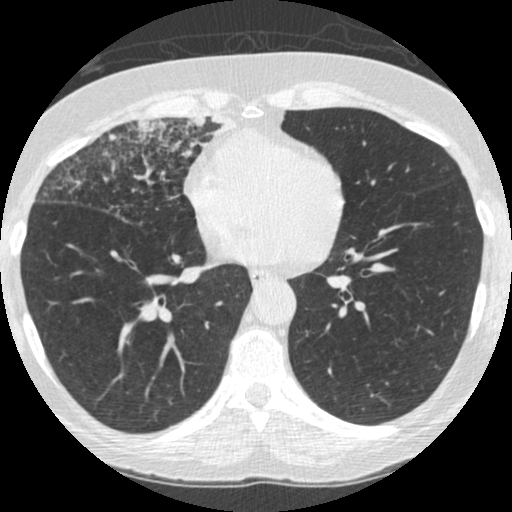
Low-dose screening chest CT, one axial slice; position 114 of 253 along the scan axis; reconstruction kernel STANDARD; lung window (W 1500 / L -600 HU); 1.25 mm slice thickness; 512 × 512 image matrix, field of view 294 × 294 mm.
Annotated regions visible in this slice (manually delineated by an expert):
- lesion 4 (tumor, upper lobe of right lung): bounding box (x1, y1, x2, y2) in pixels: (187, 117, 232, 149)